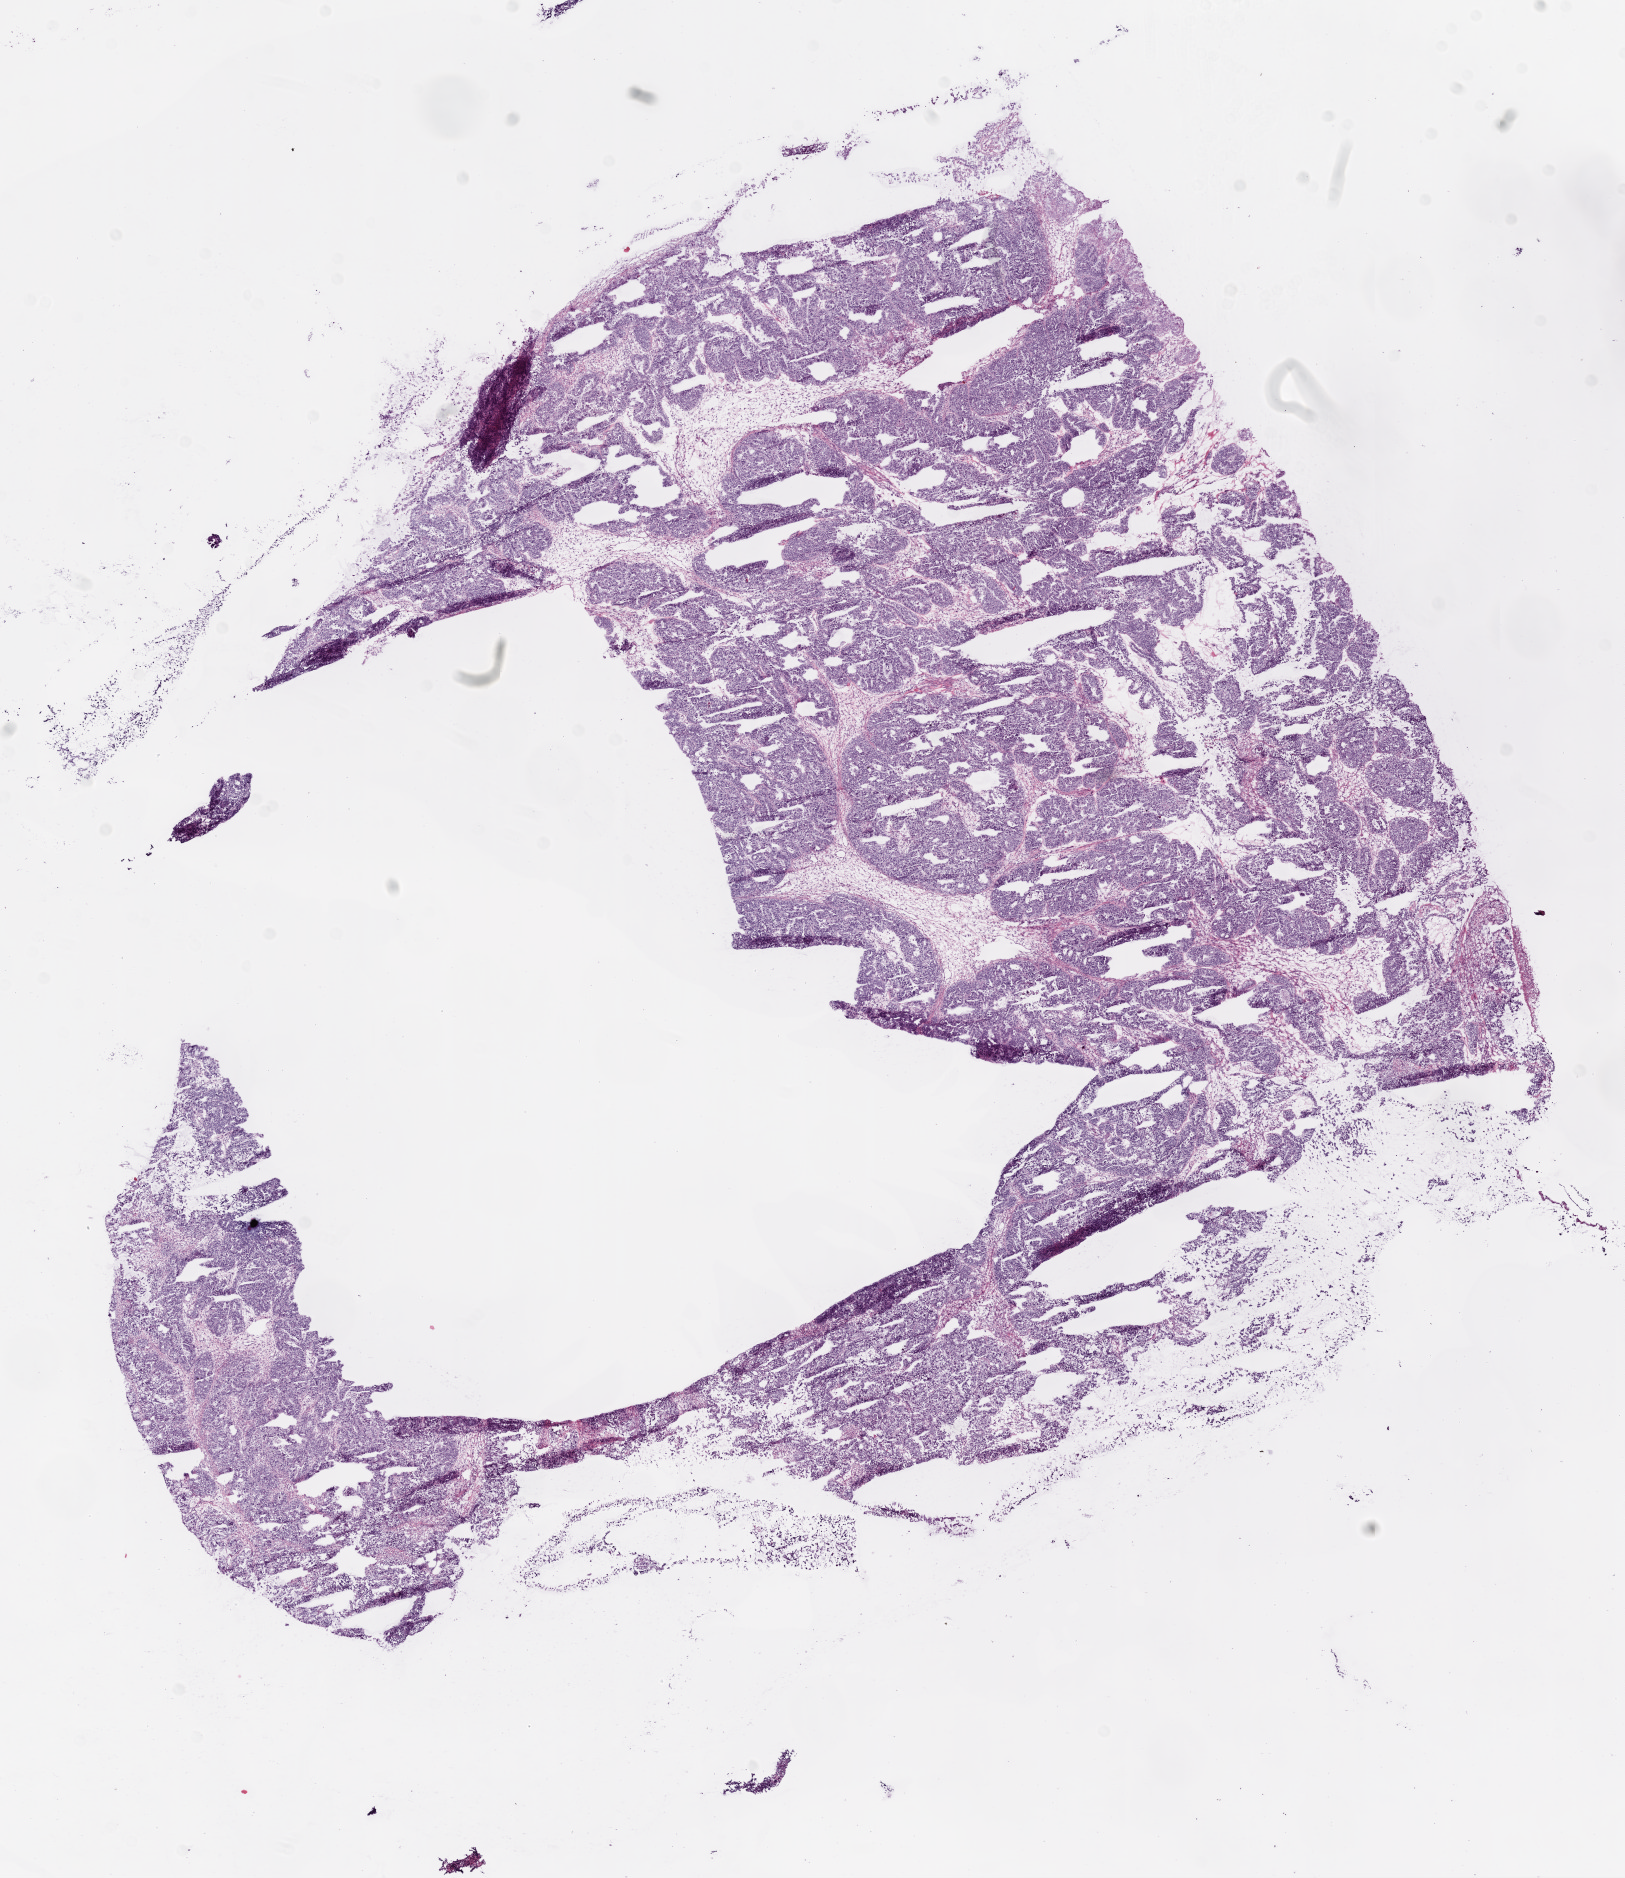
Whole-slide histology image, H&E-stained, a low-resolution overview of the entire scanned area, about 13.0 x 15.1 mm, frozen section from the bottom of the tissue portion, primary tumour sample from the ovary. Female, age 52 years at initial diagnosis. Histologic grade: G3 (poorly differentiated). Slide review estimates, as recorded: tumour cells 95%, tumour nuclei 99%, normal cells 0%, stromal cells 5%, necrosis 0%.
FIGO stage: IC. Laterality: bilateral. Diagnosis: Serous cystadenocarcinoma, NOS.